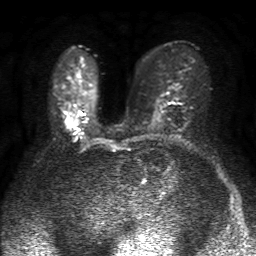
Breast MRI, one axial slice. Position 28 of 50 along the scan axis. Diffusion-weighted series; image 2 of 4 stored at this slice position (different b-values; order by instance number). 1.5 T. 256 × 256 image matrix, field of view 320 × 320 mm. Female patient.
Structures marked on this image (expert manual segmentation):
- tumour on diffusion-weighted imaging: bounding box <68,121,72,125> (left, top, right, bottom; pixels)